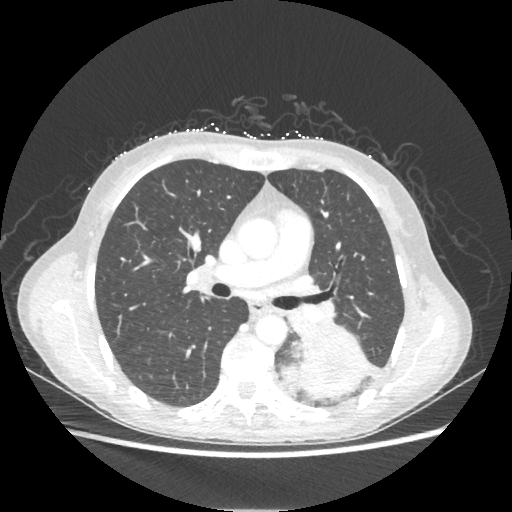
Chest CT, one axial slice. Position 125 of 221 along the scan axis. Lung window (W 1500 / L -600 HU). 1.25 mm slice thickness. 512 × 512 image matrix, field of view 360 × 360 mm. Female patient, age 53 years. Case-level facts recorded for this patient, not image findings: clinical TNM (as recorded): T3 N0 M0.
Outlined on this slice (rectangle marked by the reading radiologist):
- lung tumour (recorded histology: adenocarcinoma): box from (x=278, y=316) to (x=369, y=403) px